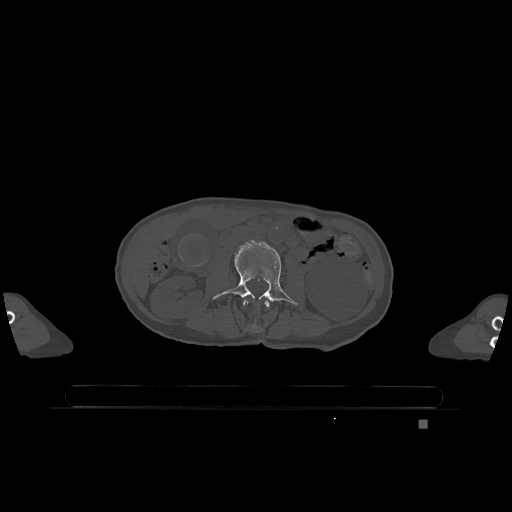
CT including the spine, one axial slice. Bone window (W 1800 / L 400 HU). 512 × 512 image matrix, field of view 500 × 500 mm. Patient: female, 74 years. Case-level facts recorded for this patient, not image findings: primary cancer: lung.
Structures marked on this image (semi-automatically segmented with operator editing):
- L2 vertebra: bounding box [x1, y1, x2, y2] px = [243, 300, 270, 329]
- L3 vertebra: [212, 241, 298, 305]